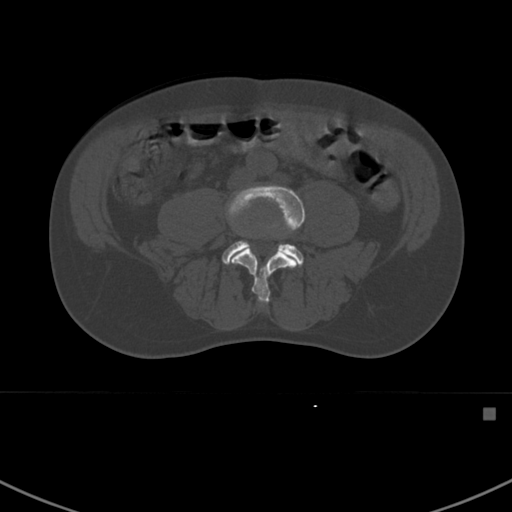
CT including the spine, one axial slice; slice 233 of 412 in the series (ordered by position); reconstruction kernel Br40s; 120 kVp; bone window (W 1800 / L 400 HU); 1.5 mm slice thickness; 512 × 512 image matrix, field of view 358 × 358 mm. Male patient, age 59 years. Case-level facts recorded for this patient, not image findings: primary cancer: prostate.
Annotated regions visible in this slice (semi-automatic segmentation, software-assisted and operator-edited):
- L4 vertebra: bounding box [x1, y1, x2, y2] px = [226, 184, 305, 304]
- L5 vertebra: [222, 241, 304, 266]